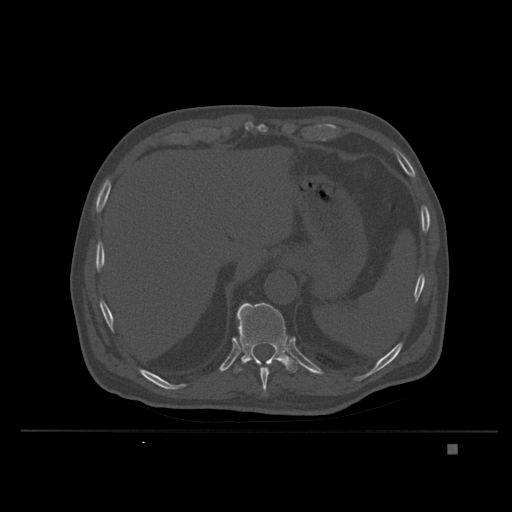
CT including the spine, one axial slice. Bone window (W 1800 / L 400 HU). 1.5 mm slice thickness. 512 × 512 image matrix. Patient: male, 73 years. From the clinical record (not read from this slice): primary cancer: skin.
Annotated regions visible in this slice (semi-automatically segmented with operator editing):
- T10 vertebra: bounding box (x1, y1, x2, y2) in pixels: (259, 364, 272, 391)
- T11 vertebra: (234, 303, 299, 373)
- T9 vertebra: (263, 391, 267, 396)